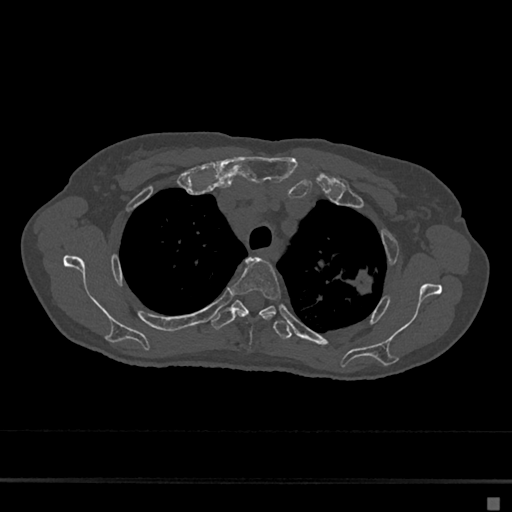
CT including the spine, one axial slice. Position 525 of 797 along the scan axis. Reconstruction kernel Br40s/3. 120 kVp. Bone window (W 1800 / L 400 HU). 0.5 mm slice thickness. 512 × 512 image matrix, field of view 360 × 360 mm. Female patient, age 68 years. From the clinical record (not read from this slice): primary cancer: renal.
Outlined on this slice (semi-automatic segmentation, software-assisted and operator-edited):
- T3 vertebra: box from (x=231, y=258) to (x=281, y=320) px
- T4 vertebra: (x=210, y=300)–(x=292, y=340)